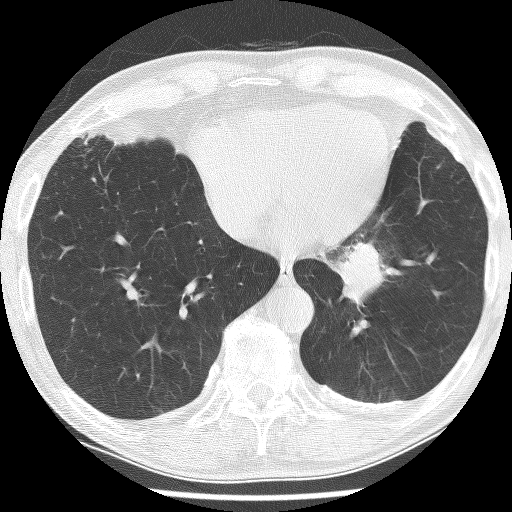
Low-dose screening chest CT, one axial slice. Position 54 of 226 along the scan axis. 120 kVp. Lung window (W 1500 / L -600 HU). 512 × 512 image matrix.
Outlined on this slice (expert manual segmentation):
- lesion 1 (tumor, lower lobe of left lung): bounding box <341,242,383,305> (left, top, right, bottom; pixels)